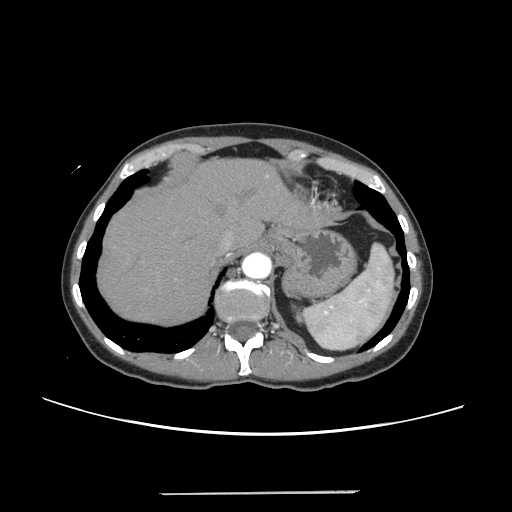
Contrast-enhanced abdominal CT, one axial slice. Position 201 of 240 along the scan axis. 120 kVp. Intravenous contrast given. Soft-tissue window (W 400 / L 40 HU). 1.25 mm slice thickness. 512 × 512 image matrix, field of view 371 × 371 mm. Female patient, age 60 years. Case-level facts recorded for this patient, not image findings: diagnosis: colorectal cancer liver metastases, imaged before liver resection; multiple liver metastases: no; largest metastasis: 1.5 cm.
Outlined on this slice (manually delineated by an expert):
- hepatic veins: bounding box (x1, y1, x2, y2) in pixels: (219, 218, 250, 252)
- liver: (98, 159, 321, 324)
- planned liver remnant (the part of the liver to remain after resection): (98, 159, 317, 324)